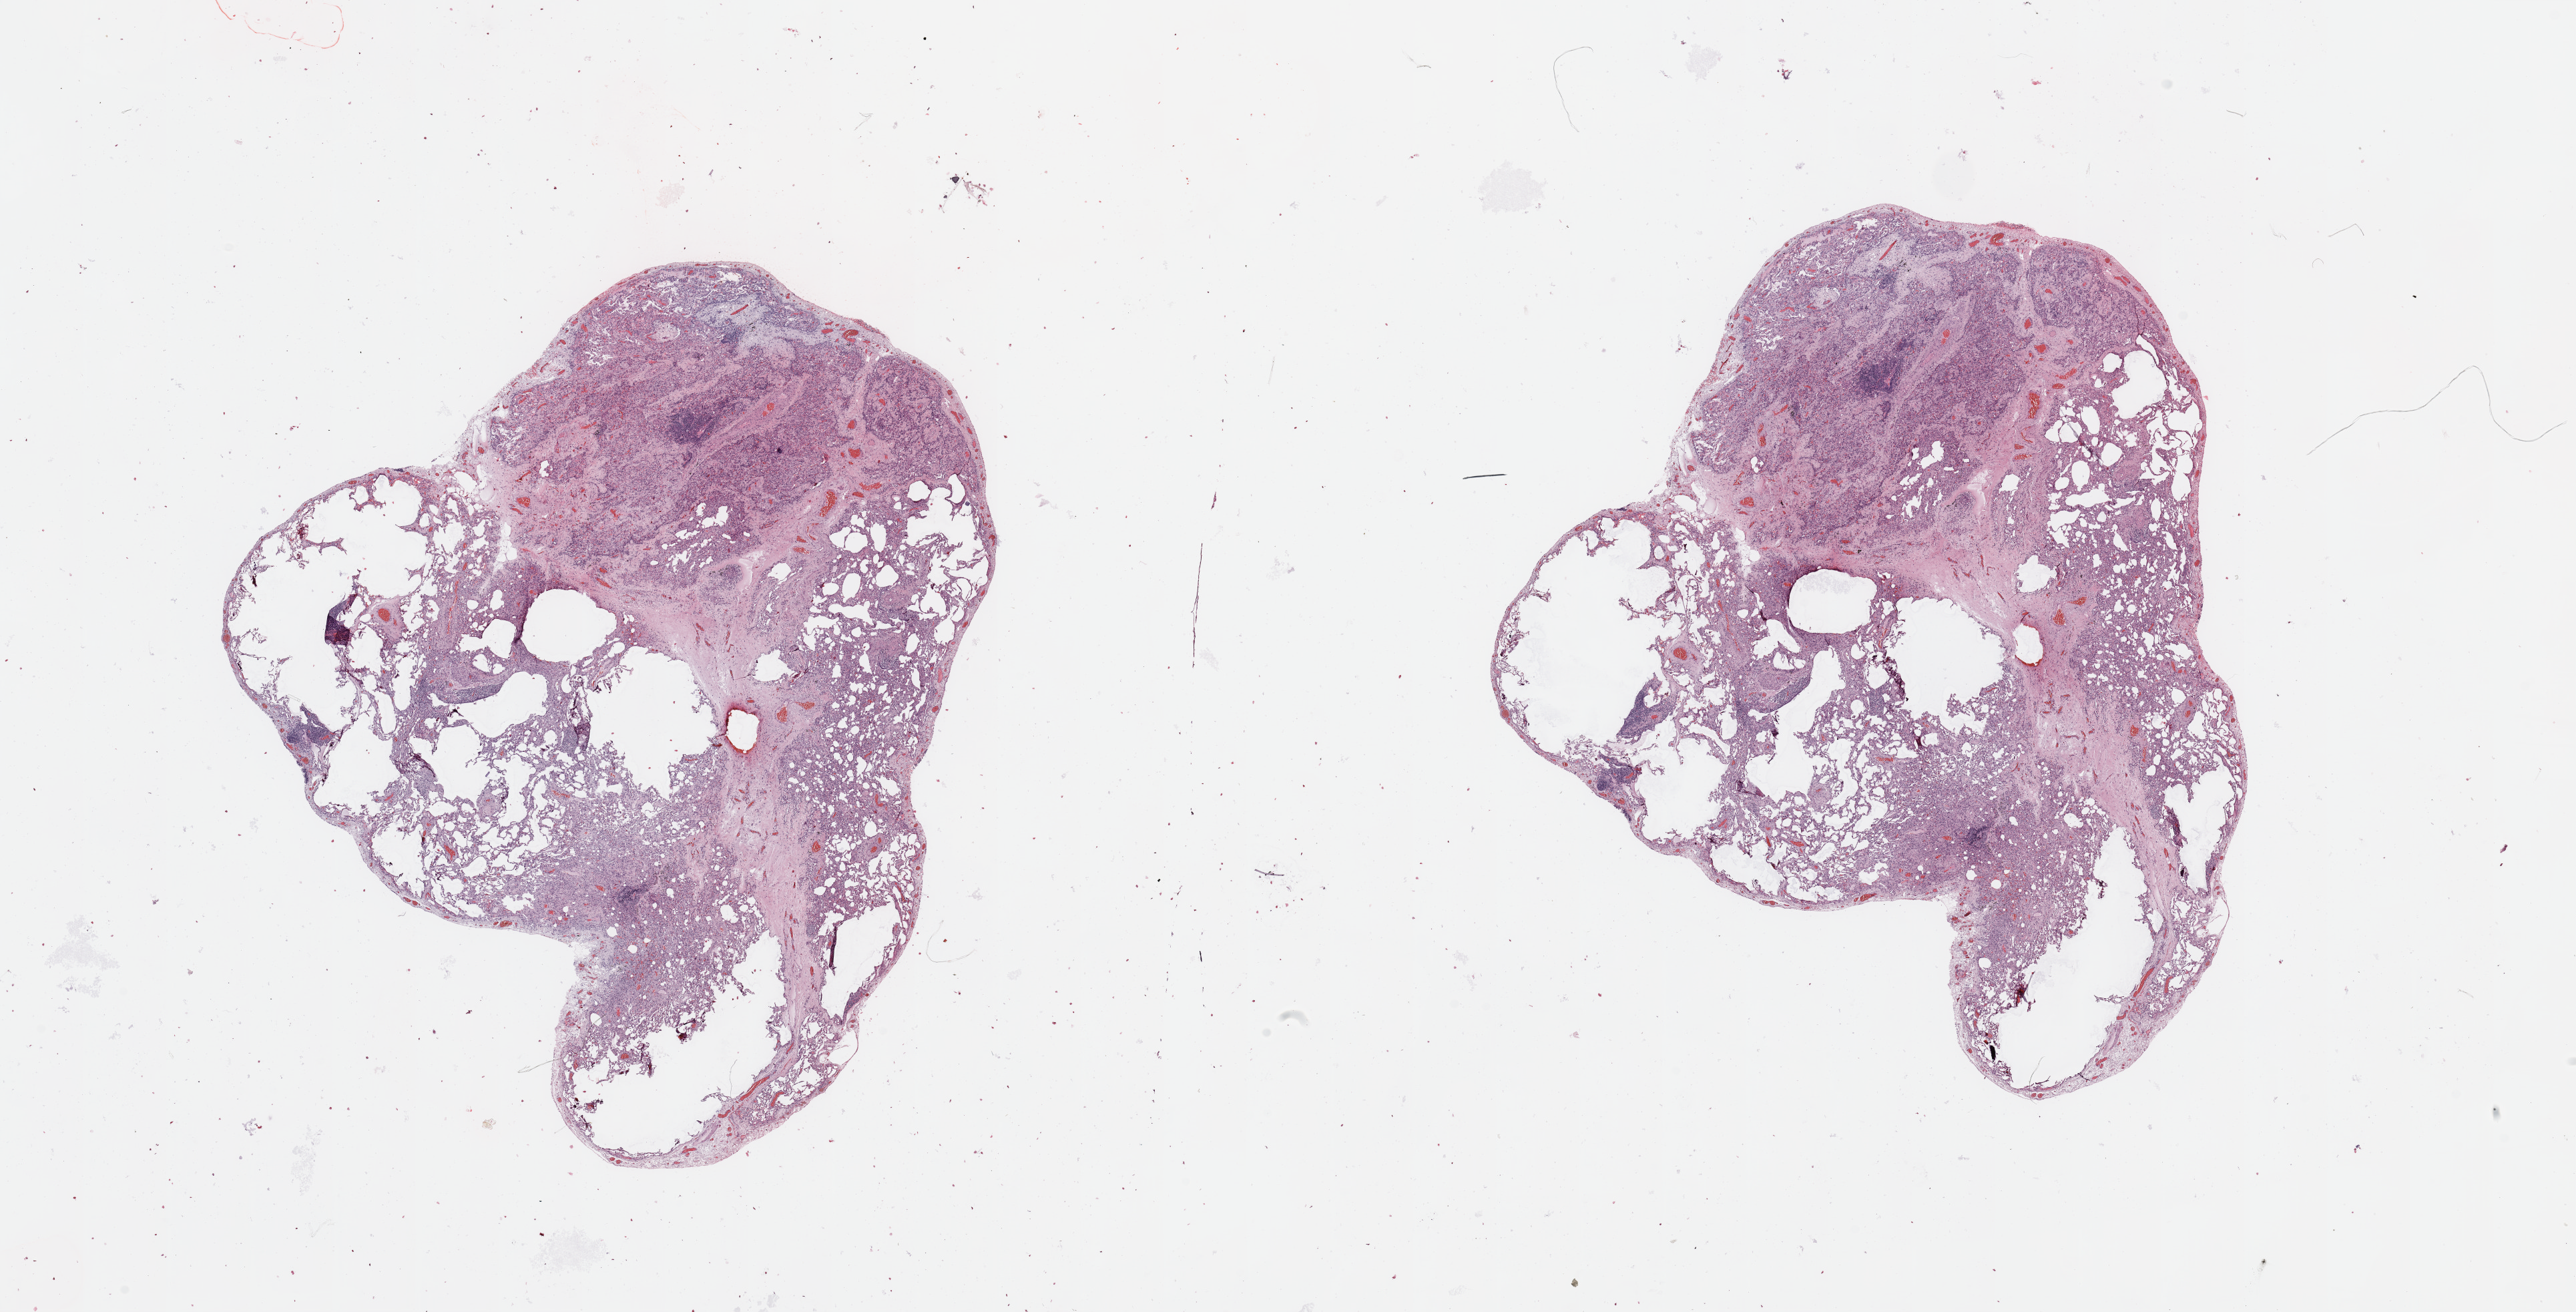
Whole-slide histology image, Hematoxylin and eosin (H&E) stained, shown as a low-resolution overview of the whole scanned area (about 30.5 x 15.5 mm, slide scanned at 20x). Normal (non-tumour) tissue sample, sampled site: lung. Patient: male, age 73 years.
This section: normal (non-tumour) tissue from the same patient. Patient diagnosis: Squamous cell carcinoma, NOS.